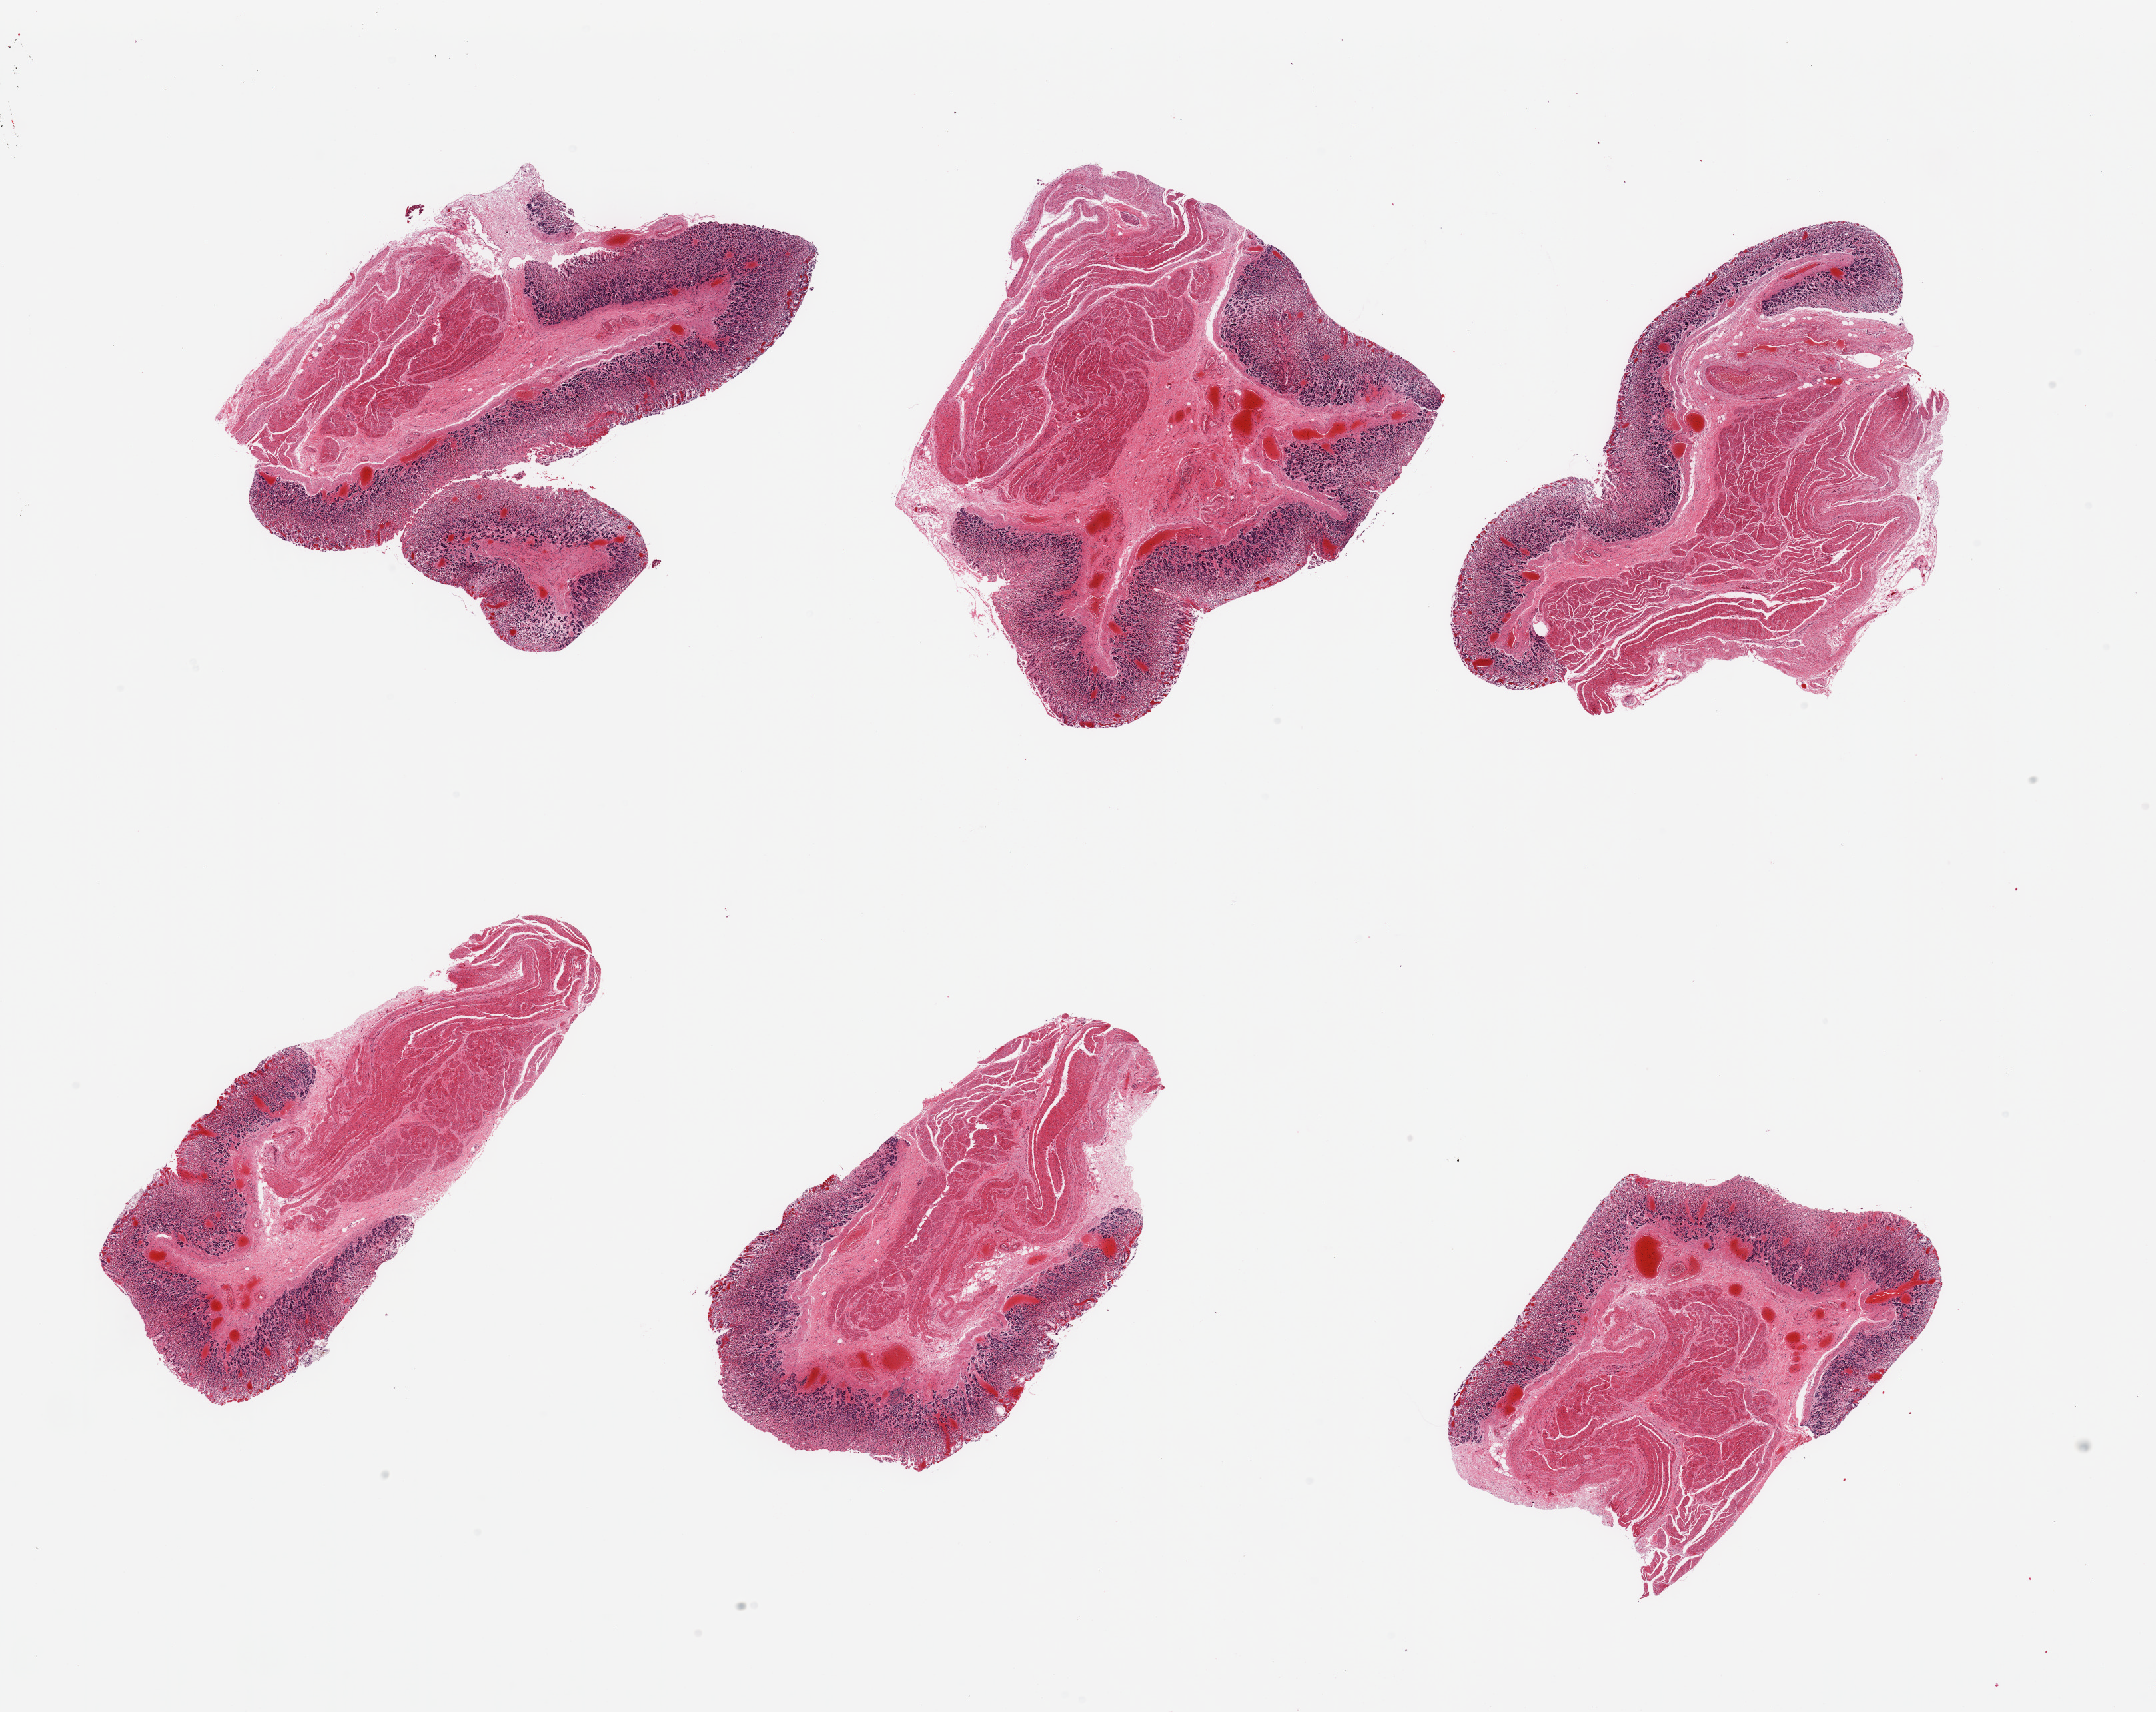
Whole-slide image, haematoxylin and eosin stain, a low-resolution overview of the entire scanned area, about 25.6 x 20.3 mm (acquisition: 20x scan); PAXgene-fixed paraffin-embedded (PFPE) section; section of stomach (target tissue); tissue donor sample. Donor sex: male.
Review note (as recorded): 6 pieces, mucosa up to ~0,8mm, moderate-advanced autolysis.